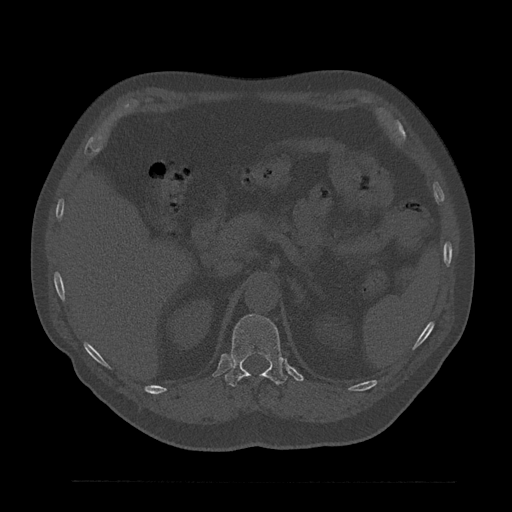
CT including the spine, one axial slice; slice 237 of 797 in the series (ordered by position); bone window (W 1800 / L 400 HU); 0.5 mm slice thickness; 512 × 512 image matrix, field of view 430 × 430 mm. Male patient, age 61 years. From the clinical record (not read from this slice): primary cancer: prostate.
Structures marked on this image (semi-automatic segmentation, software-assisted and operator-edited):
- T12 vertebra: bounding box [x1, y1, x2, y2] px = [225, 314, 287, 387]